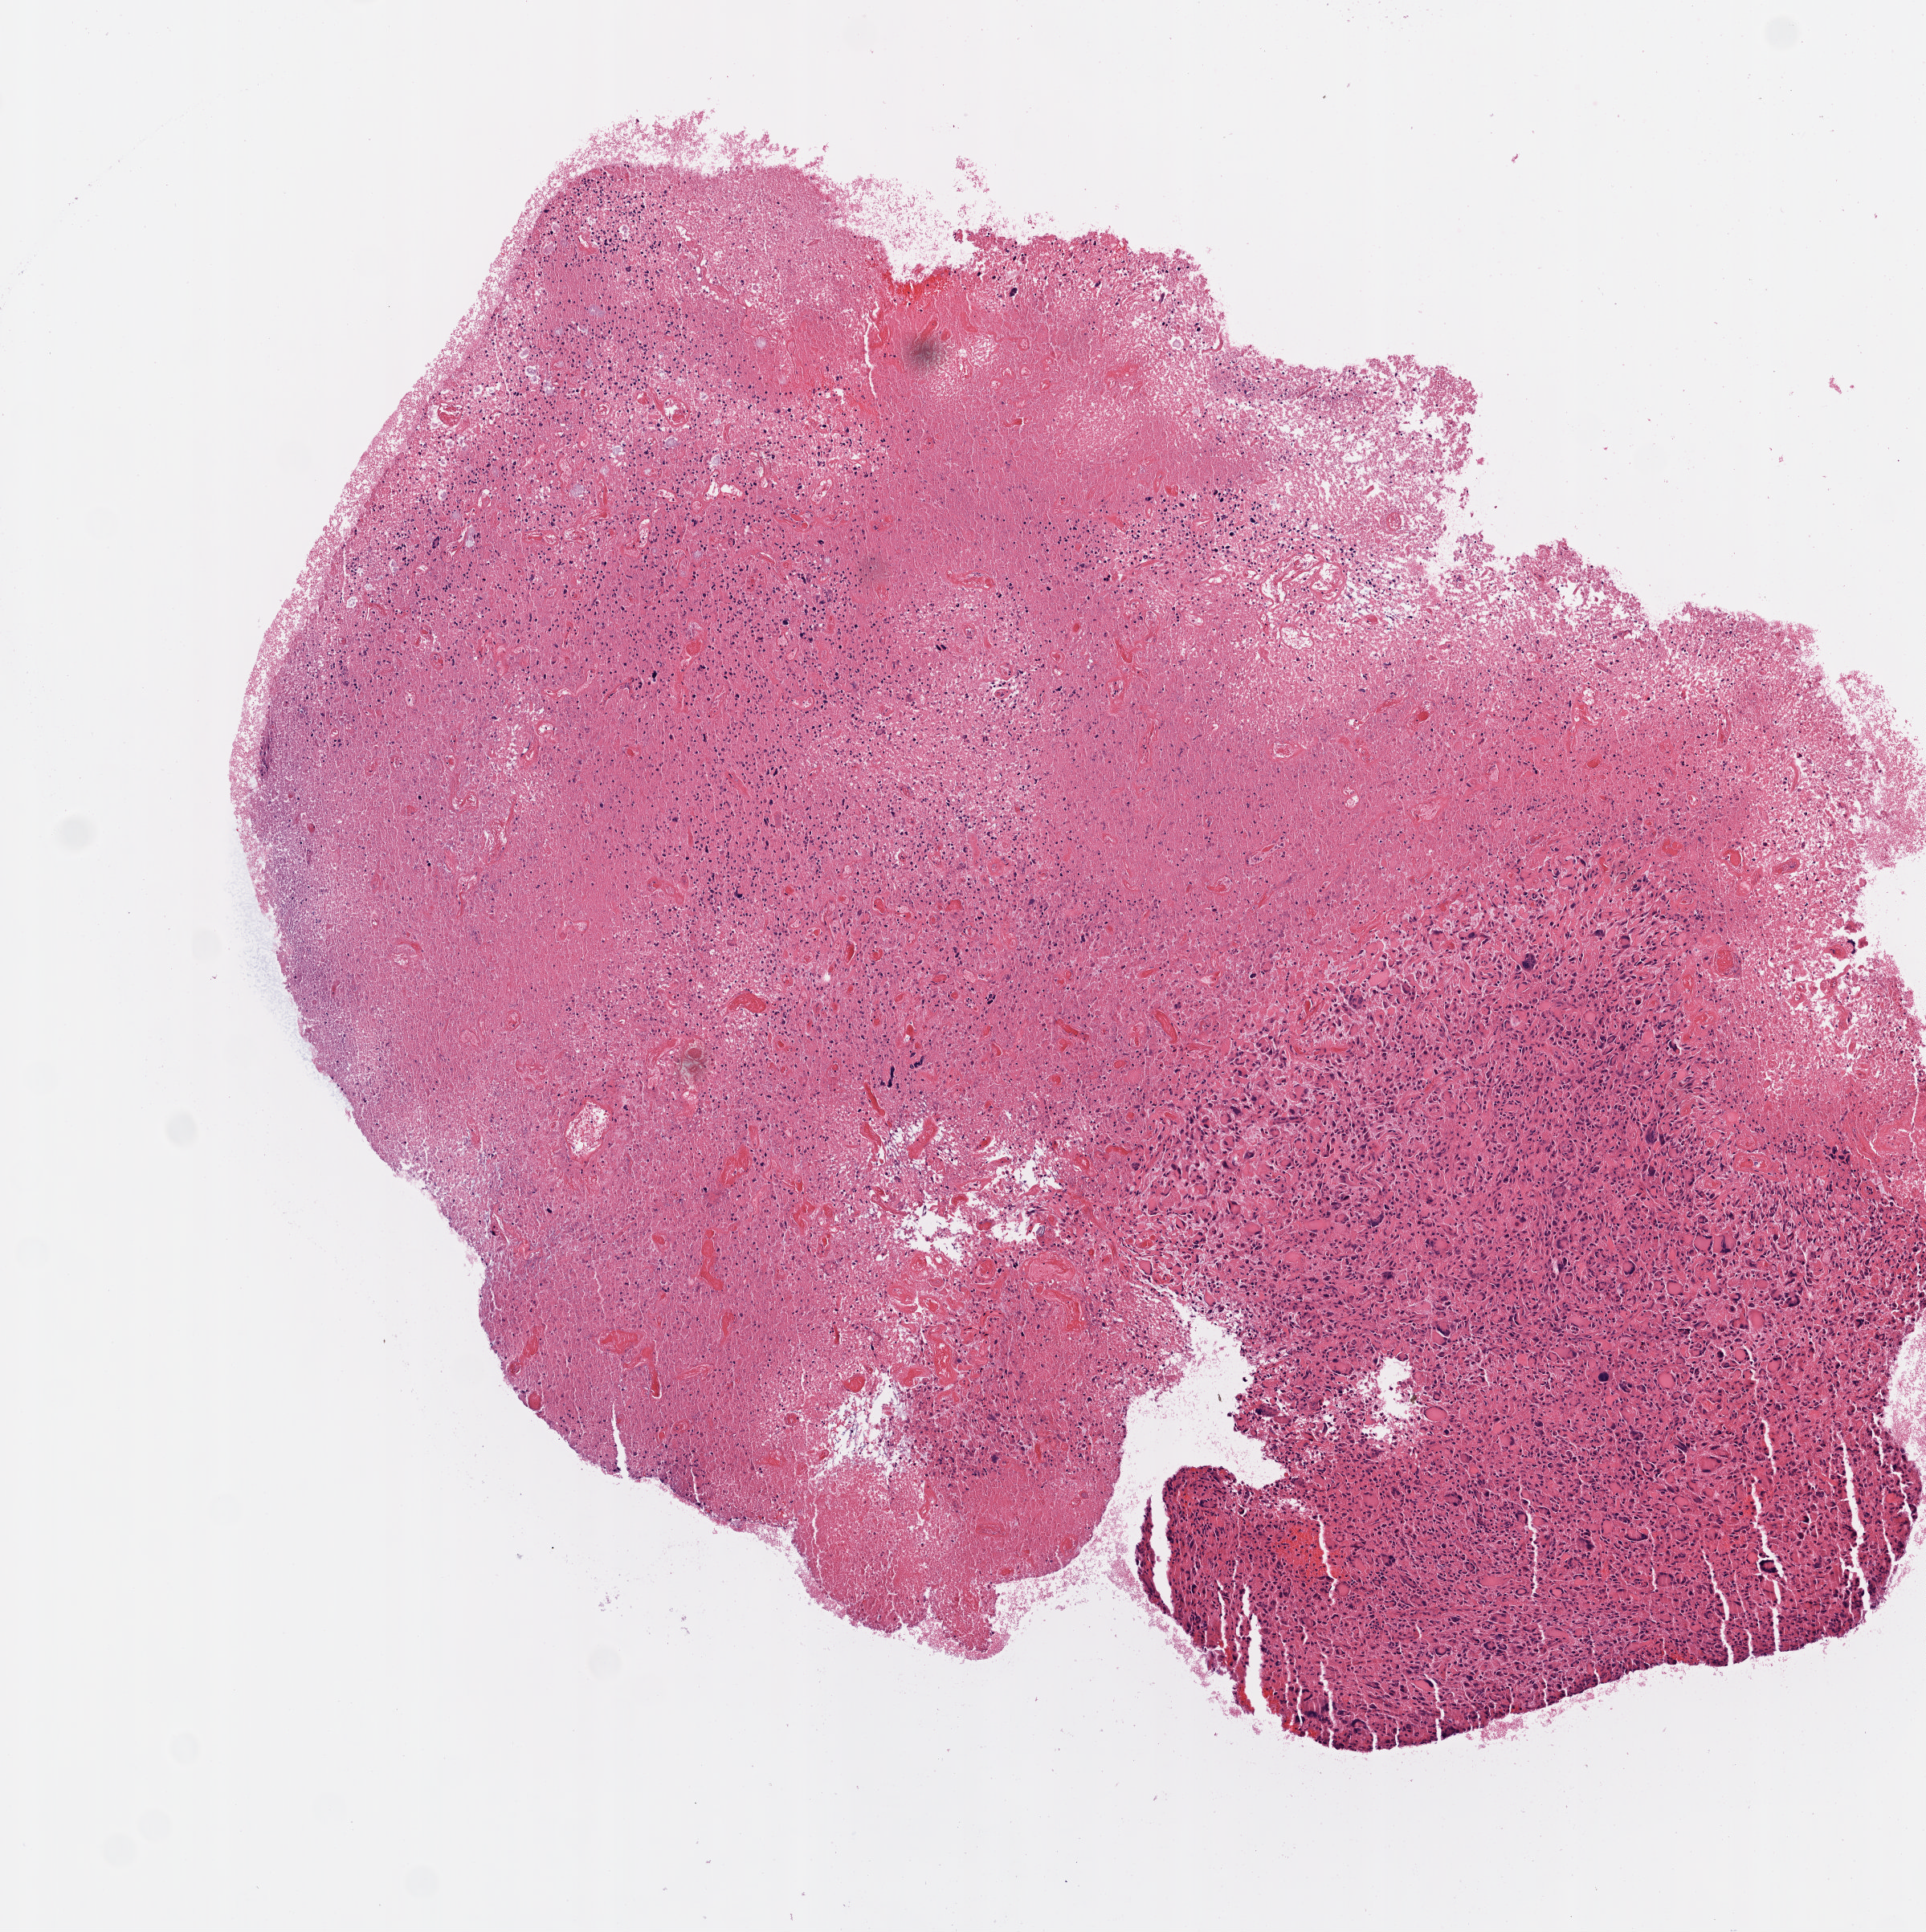
Whole-slide histology image, Hematoxylin and eosin (H&E) stained — whole scanned area (about 4.8 x 4.9 mm, acquisition: 20x scan) shown as a low-resolution overview; formalin-fixed paraffin-embedded (FFPE) diagnostic section; sample: primary tumour, brain. Female patient; age at initial diagnosis 55 years.
Pathologic diagnosis: Glioblastoma.